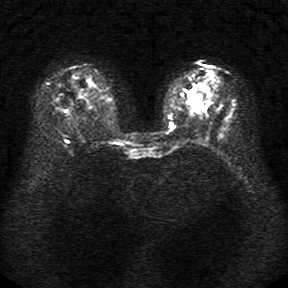
Breast MRI, one axial slice; position 14 of 34 along the scan axis; diffusion-weighted series; image 2 of 4 stored at this slice position (different b-values; order by instance number); 1.5 T; 5 mm slice thickness; 288 × 288 image matrix, field of view 340 × 340 mm. Female patient.
Outlined on this slice (manually delineated by an expert):
- tumour on diffusion-weighted imaging: bounding box <192,95,202,107> (left, top, right, bottom; pixels)